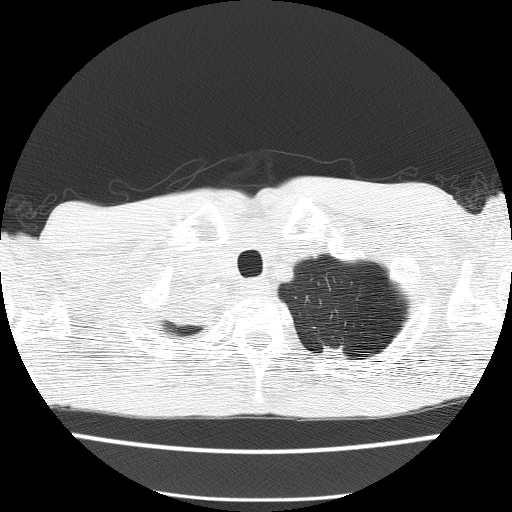
Low-dose screening chest CT, one axial slice; reconstruction kernel FC51; 120 kVp; lung window (W 1500 / L -600 HU); 2 mm slice thickness; 512 × 512 image matrix.
Outlined on this slice (manually delineated by an expert):
- lesion 1 (tumor, hilum of right lung): bounding box (x1, y1, x2, y2) in pixels: (169, 290, 211, 325)